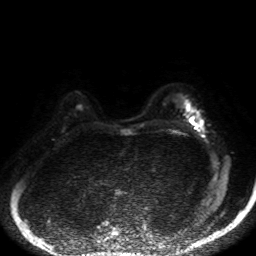
Breast MRI, one axial slice; position 34 of 50 along the scan axis; diffusion-weighted series; image 2 of 4 stored at this slice position (different b-values; order by instance number); 1.5 T; 4 mm slice thickness; 256 × 256 image matrix. Female patient.
Annotated regions visible in this slice (expert manual segmentation):
- tumour on diffusion-weighted imaging: bounding box (x1, y1, x2, y2) in pixels: (190, 117, 196, 124)